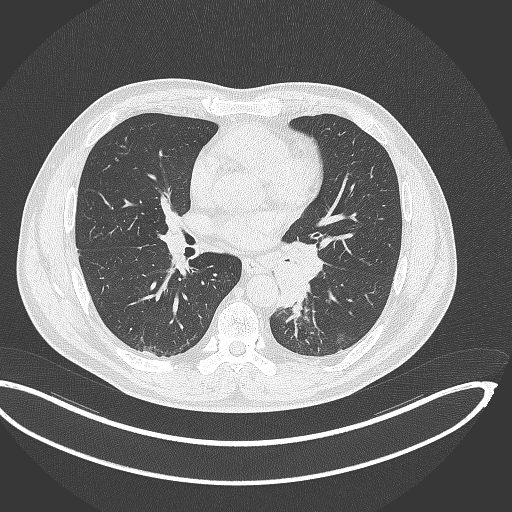
Chest CT, one axial slice. Position 179 of 362 along the scan axis. Reconstruction kernel B70f. 120 kVp. Lung window (W 1500 / L -600 HU). 1 mm slice thickness. 512 × 512 image matrix, field of view 442 × 442 mm. Male patient, age 50 years. From the clinical record (not read from this slice): clinical TNM (as recorded): T2a N3 M0.
Outlined on this slice (bounding box drawn by a radiologist):
- lung tumour (recorded histology: squamous cell carcinoma): bounding box [x1, y1, x2, y2] px = [270, 233, 324, 312]